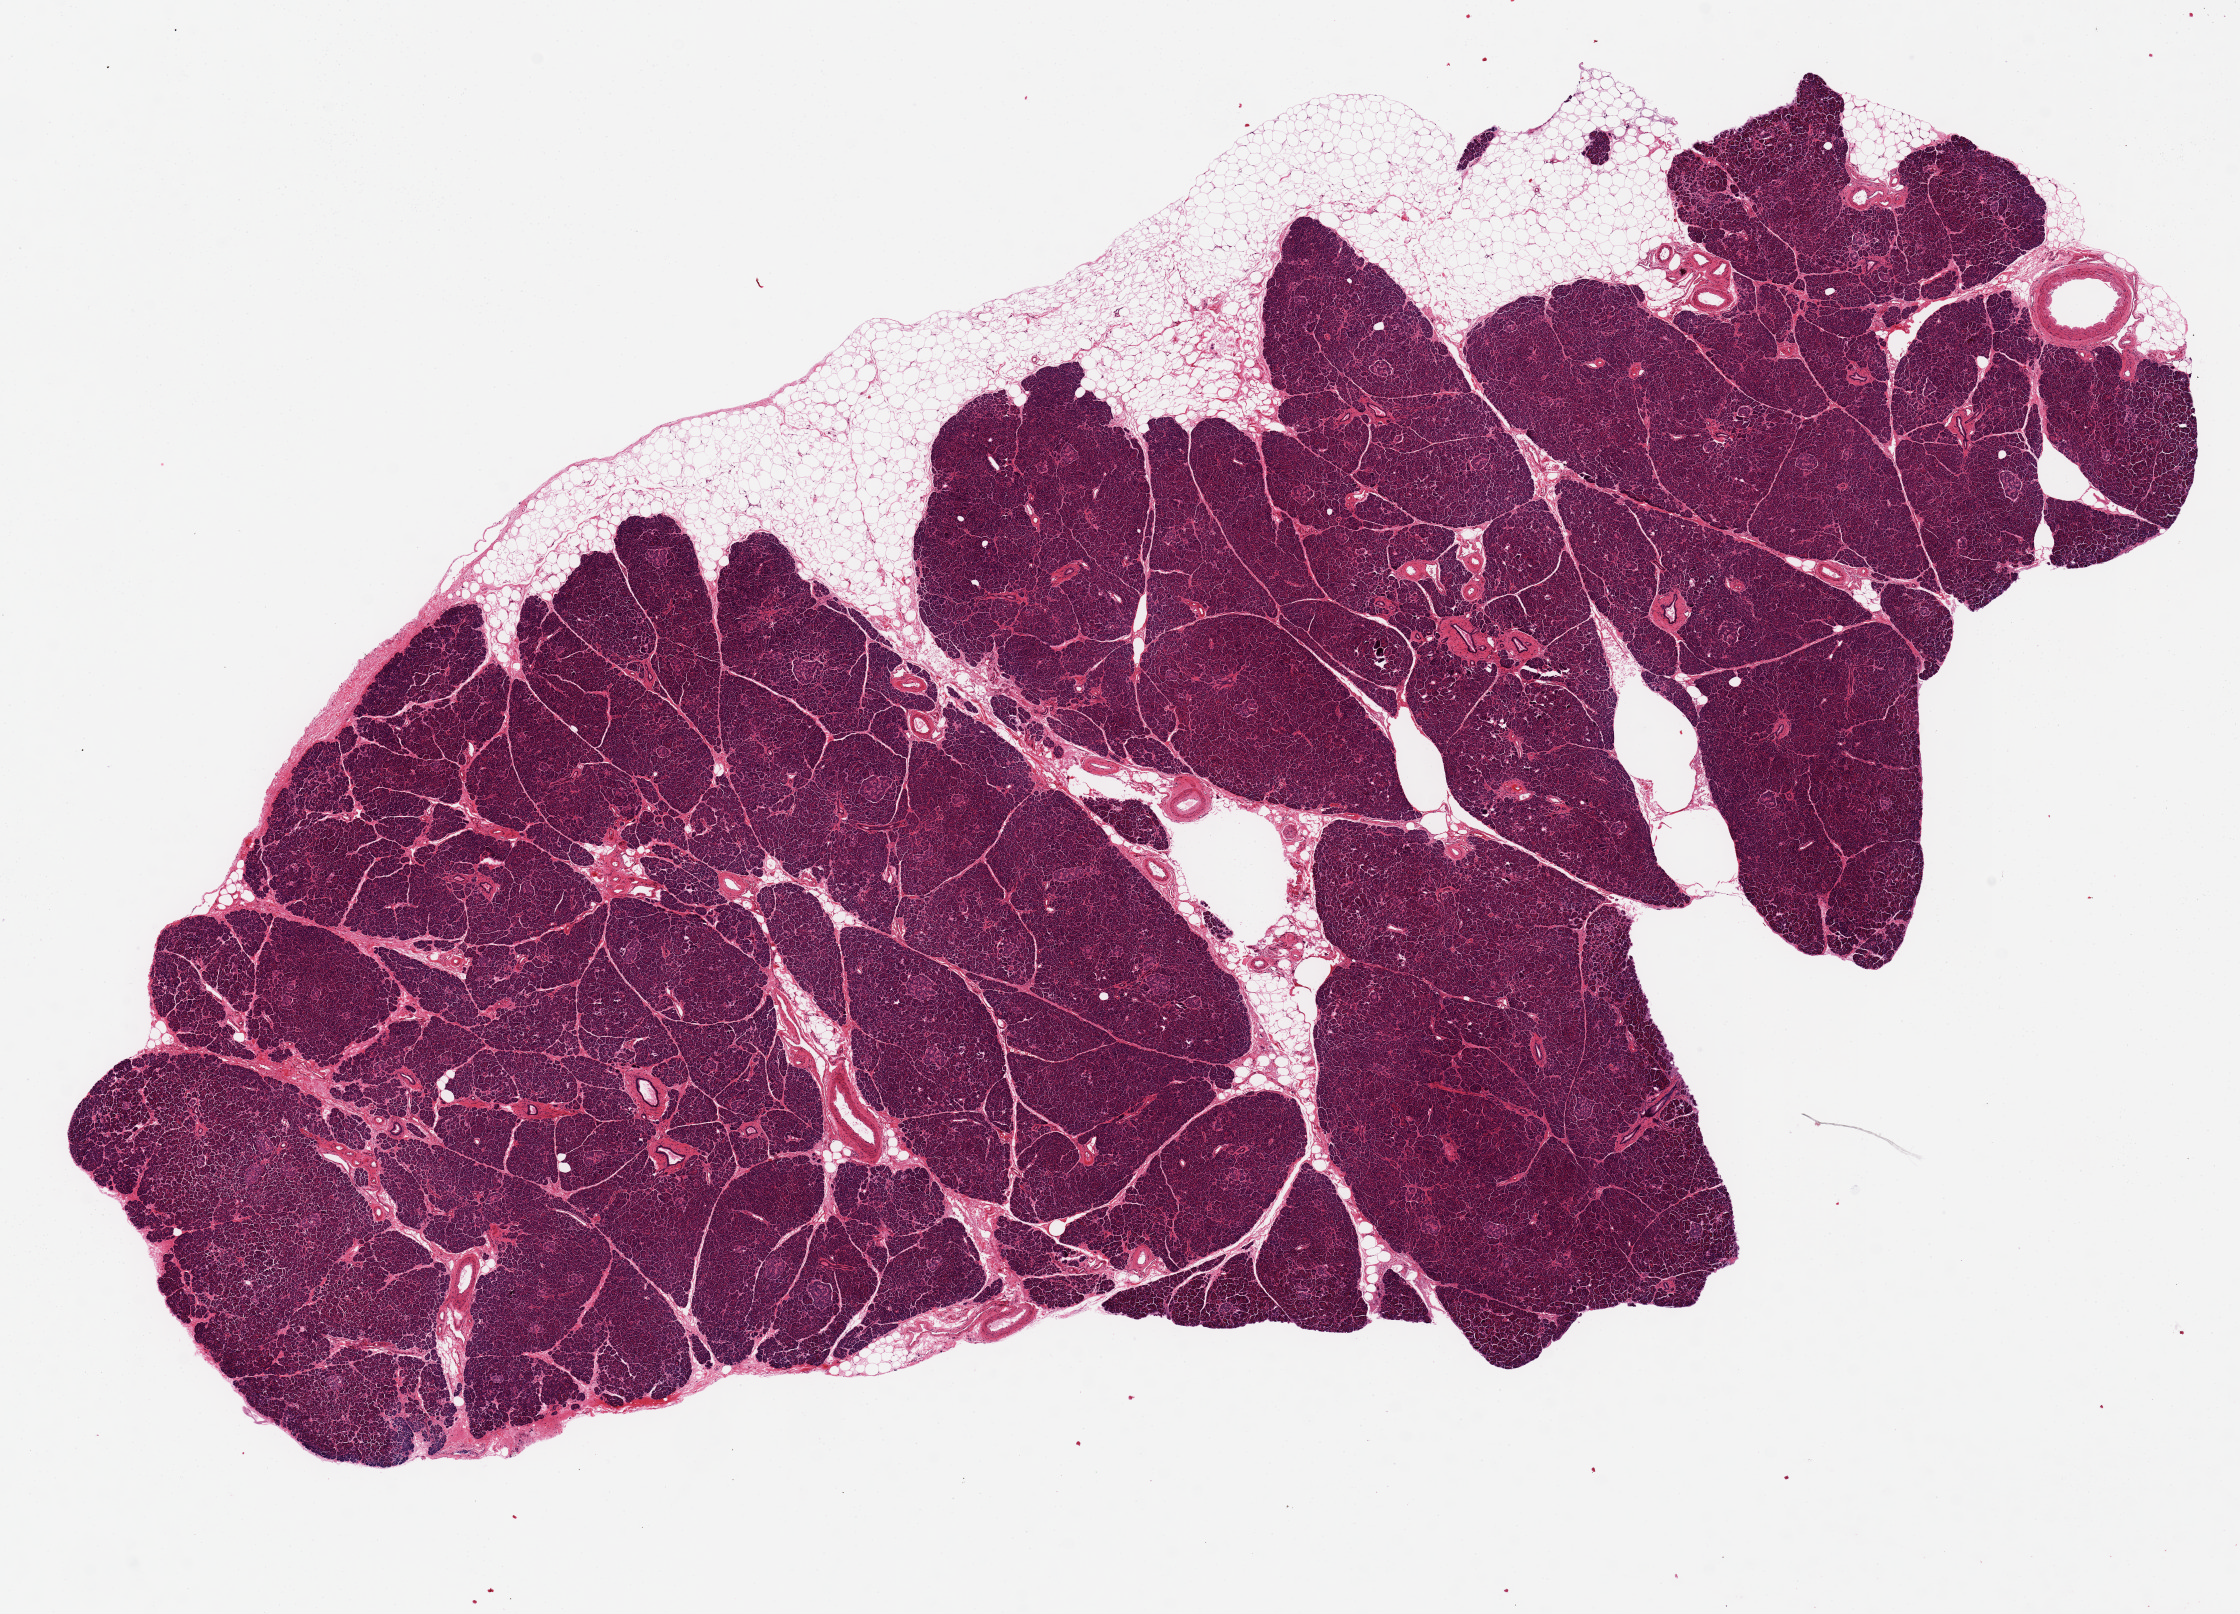
Digitized hematoxylin and eosin (H&E)-stained section, a low-resolution overview of the entire scanned area, about 17.7 x 12.8 mm (acquisition: 20x scan); PAXgene-fixed paraffin-embedded (PFPE) section; section of pancreas (target tissue); donor tissue sample. Donor: male.
* review note (as recorded): Remarkably well-preserved; good islets